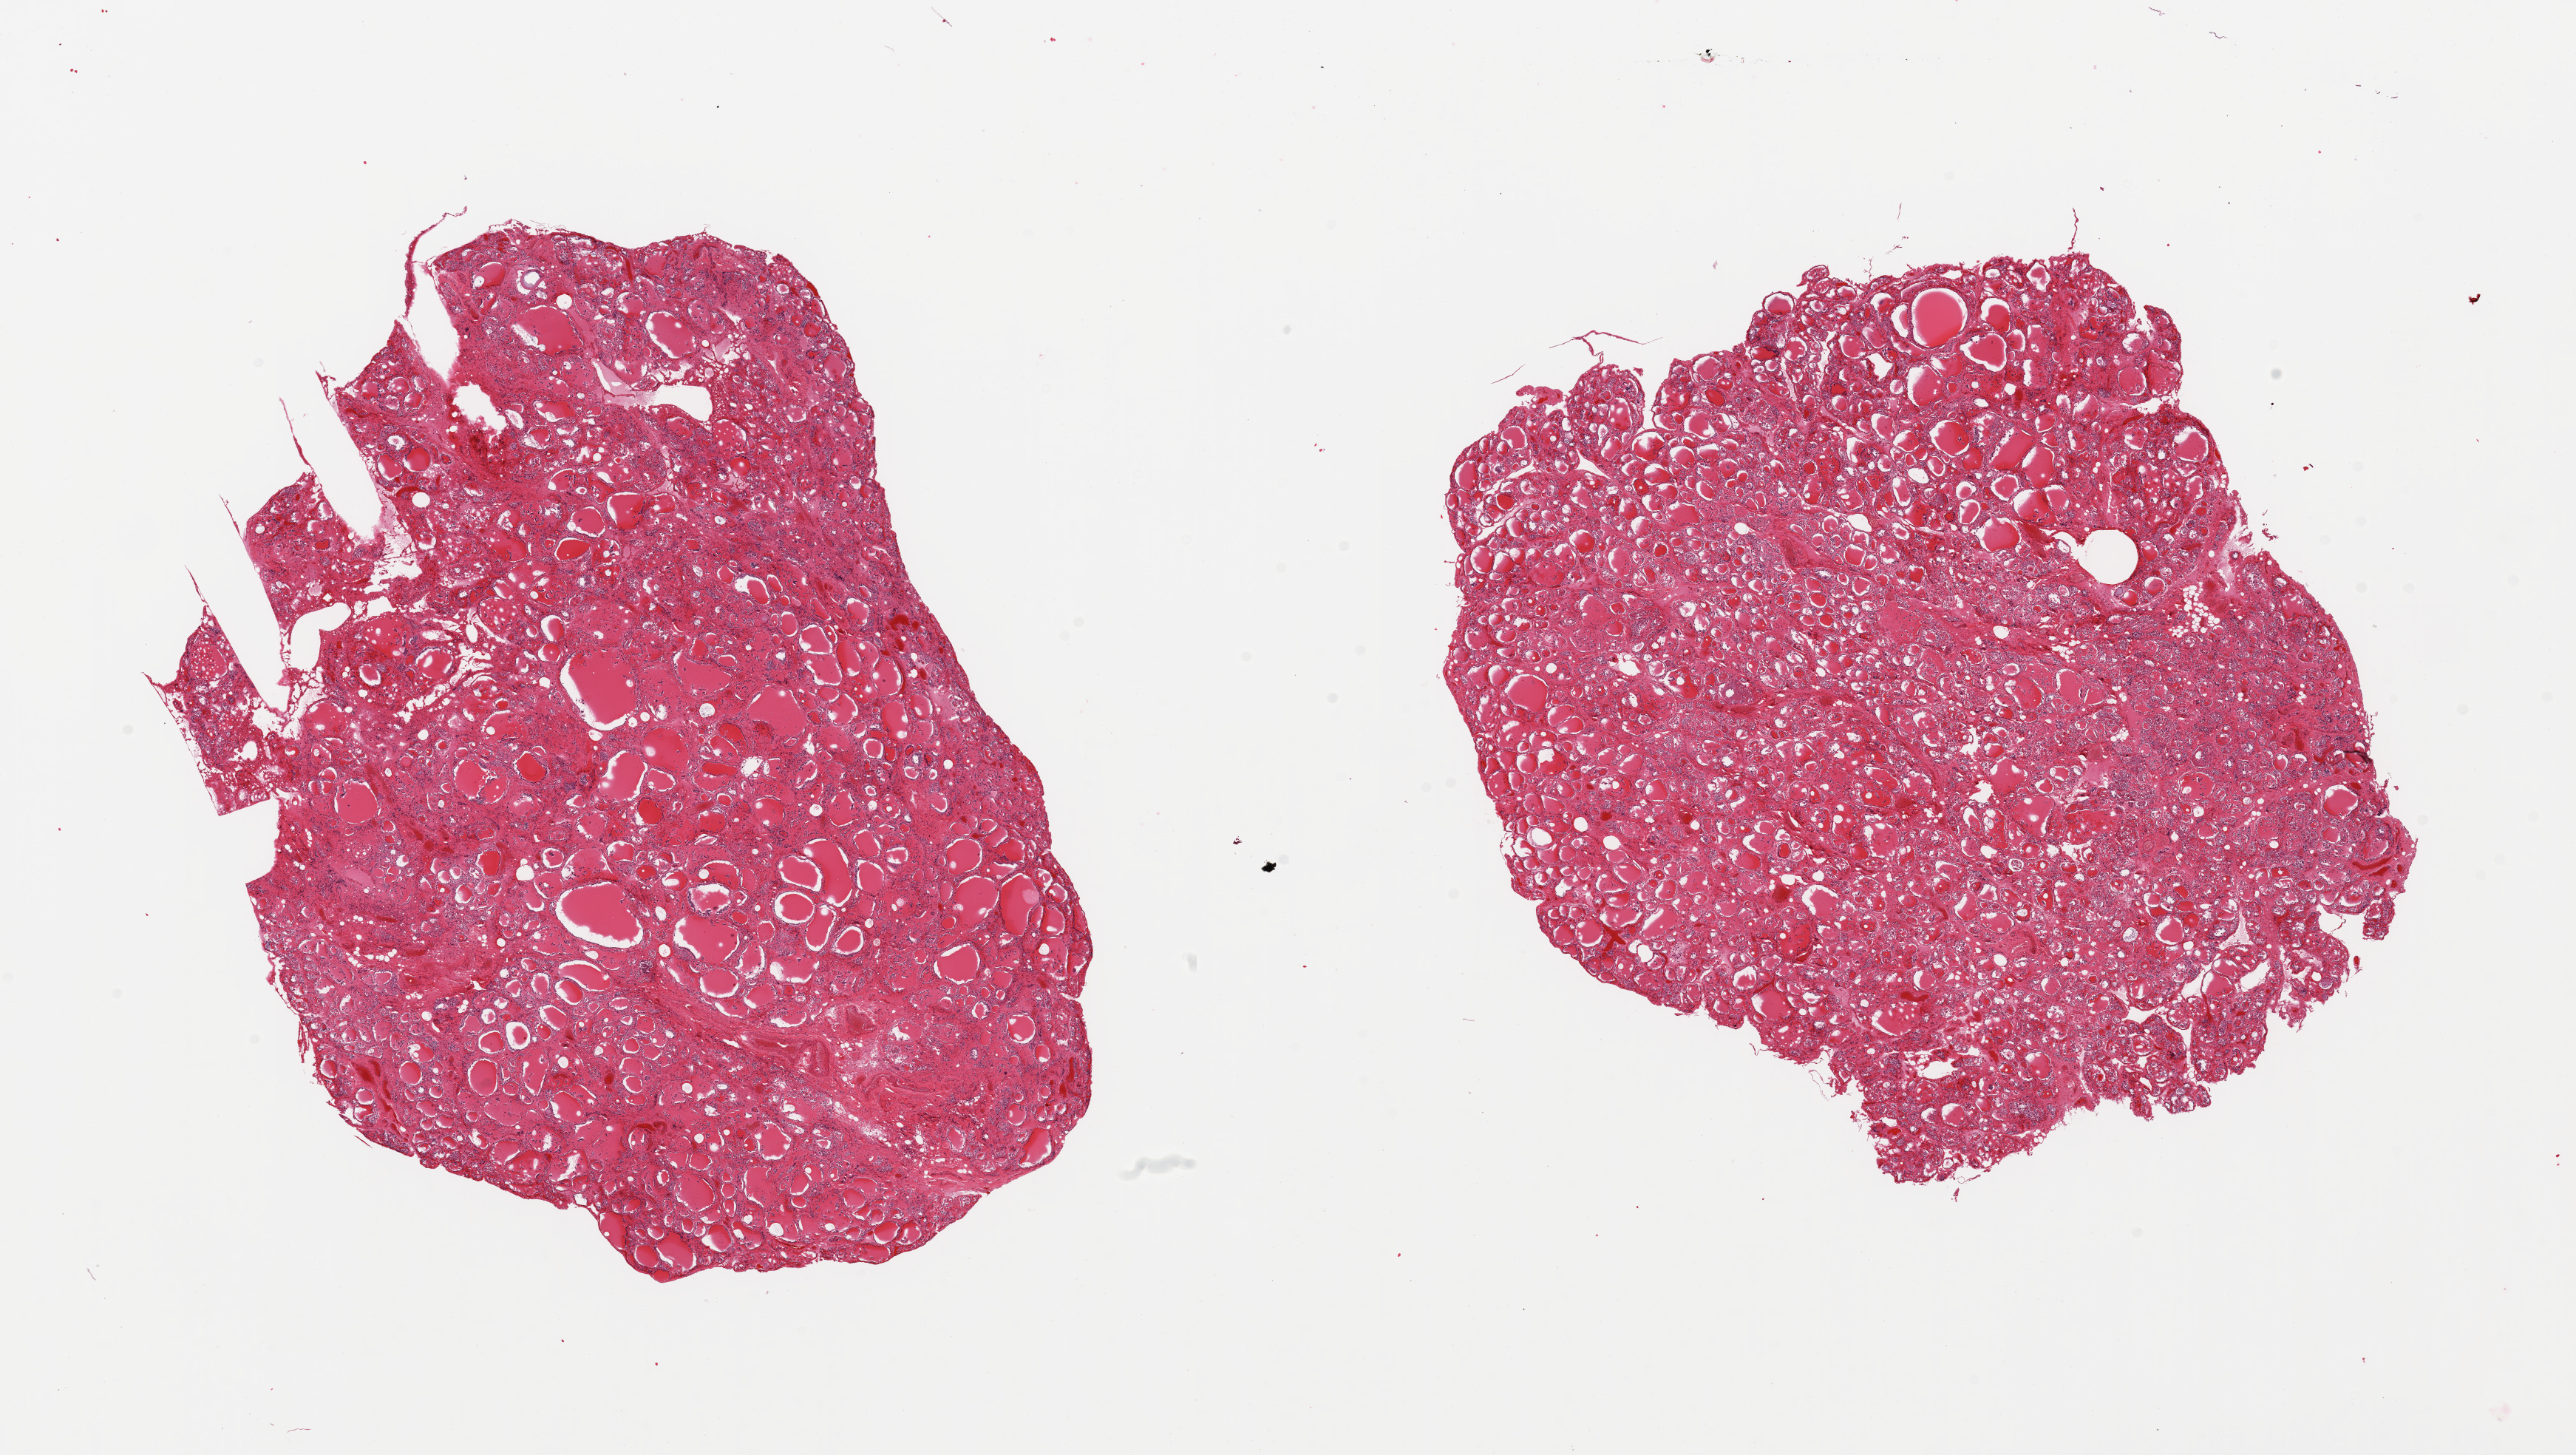
Whole-slide image, hematoxylin and eosin (H&E) stain, brightfield — whole scanned area (about 27.6 x 15.6 mm) shown as a low-resolution overview, PAXgene-fixed paraffin-embedded (PFPE) section, section of thyroid (target tissue), tissue donor sample.
Review note (as recorded): 2 pieces, no abnormalities.